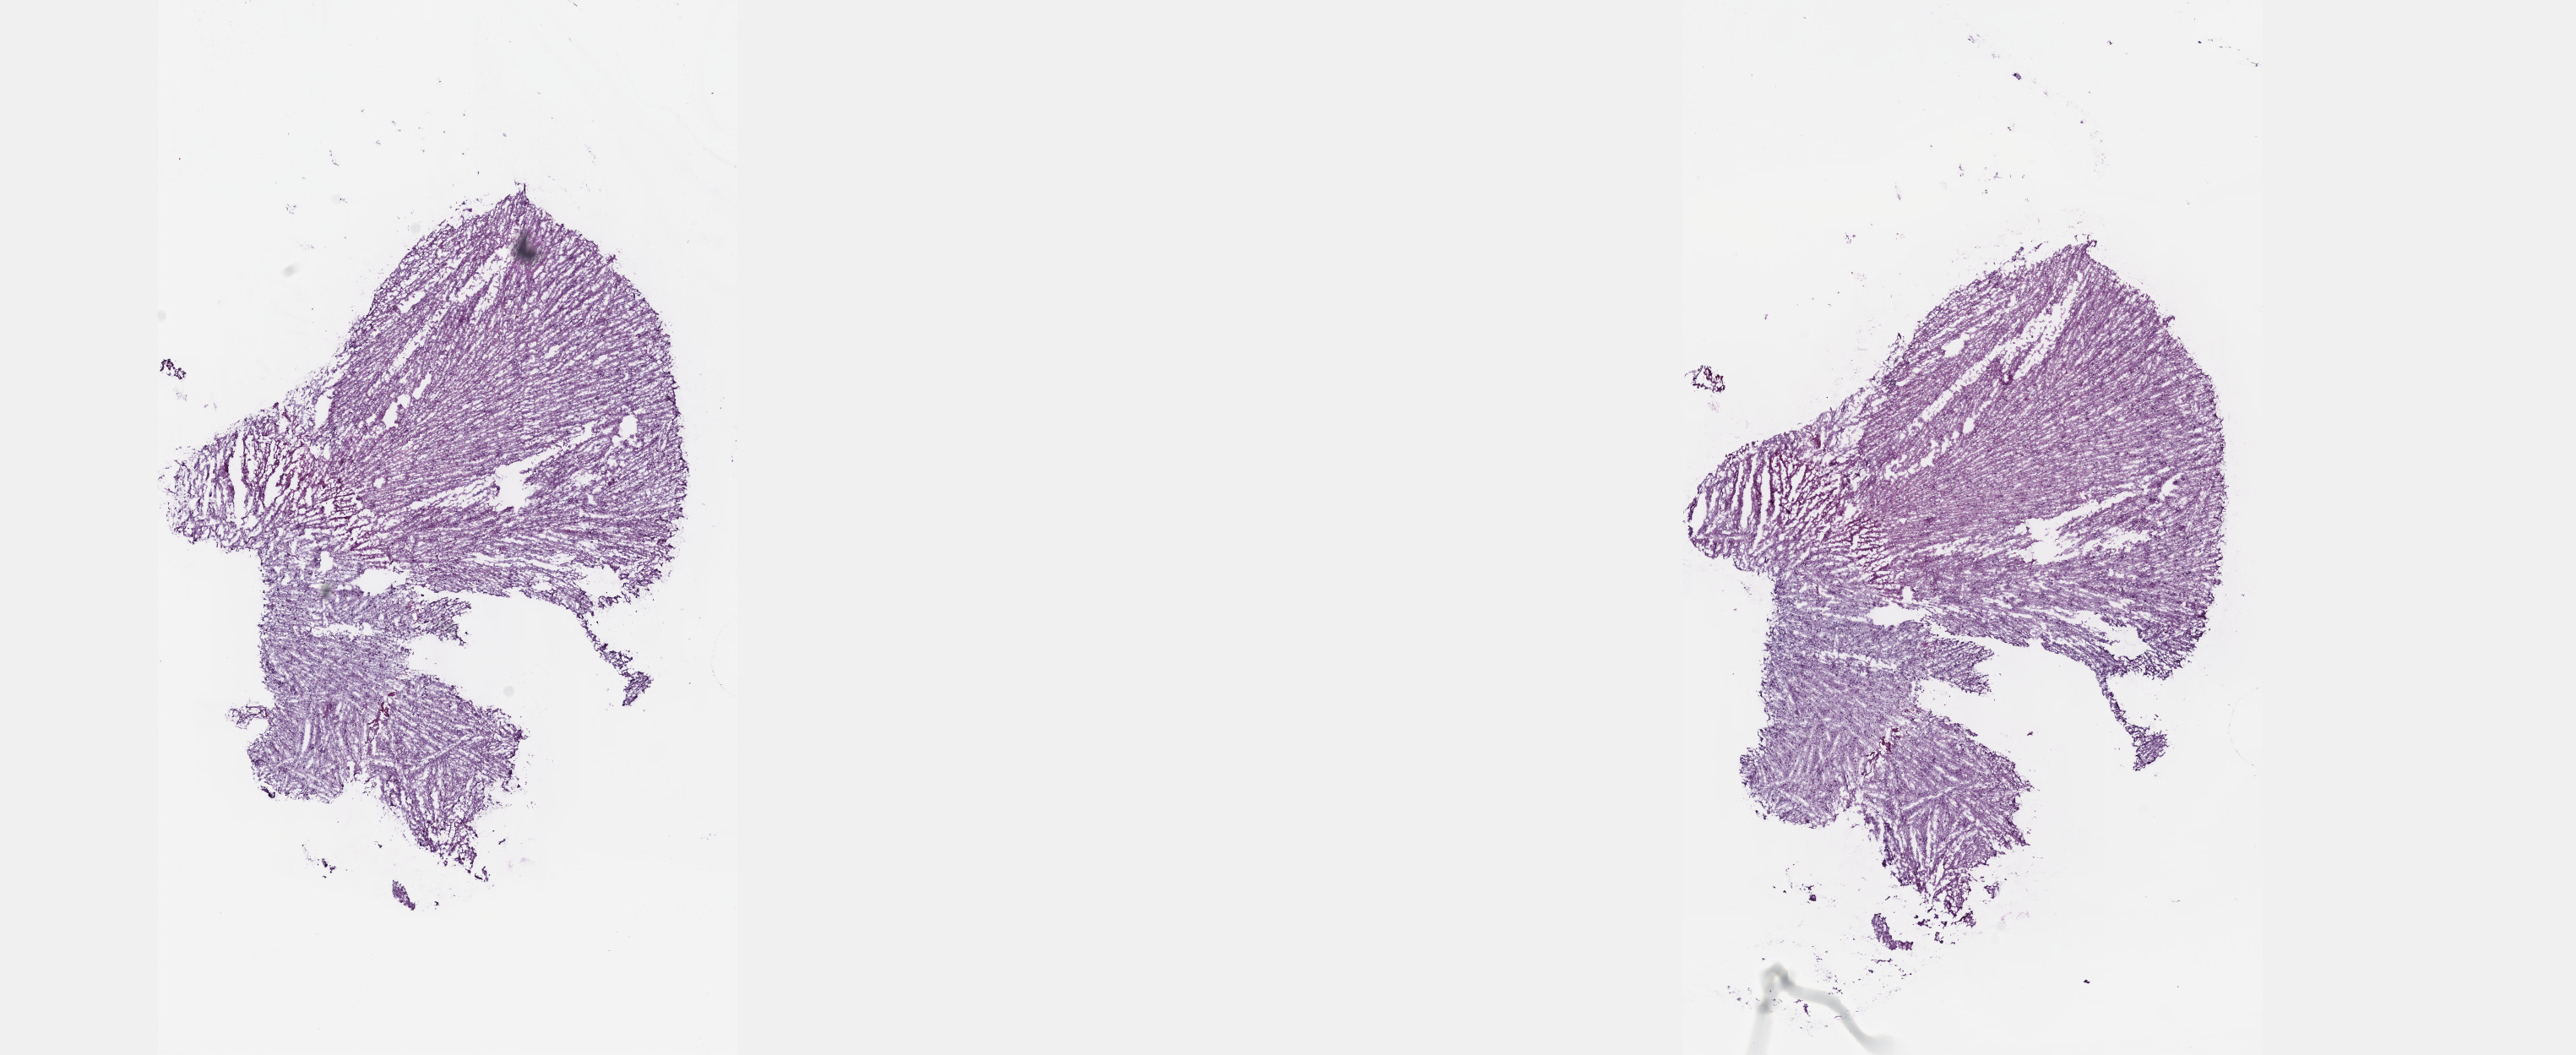
Hematoxylin and eosin (H&E) stained whole-slide image, a low-resolution overview of the entire scanned area, about 24.6 x 10.1 mm; frozen section from the top of the tissue portion; sample: primary tumour, brain. Male, age 48 years at initial diagnosis. Histologic grade: G3 (poorly differentiated). Pathologist review of this section (percent, as recorded): tumour cells 45%, tumour nuclei 80%, normal cells 10%, stromal cells 45%, necrosis 0%. Inflammatory infiltration, as recorded: lymphocyte infiltration 0%, monocyte infiltration 0%, neutrophil infiltration 0%.
Pathologic diagnosis: Astrocytoma, anaplastic.